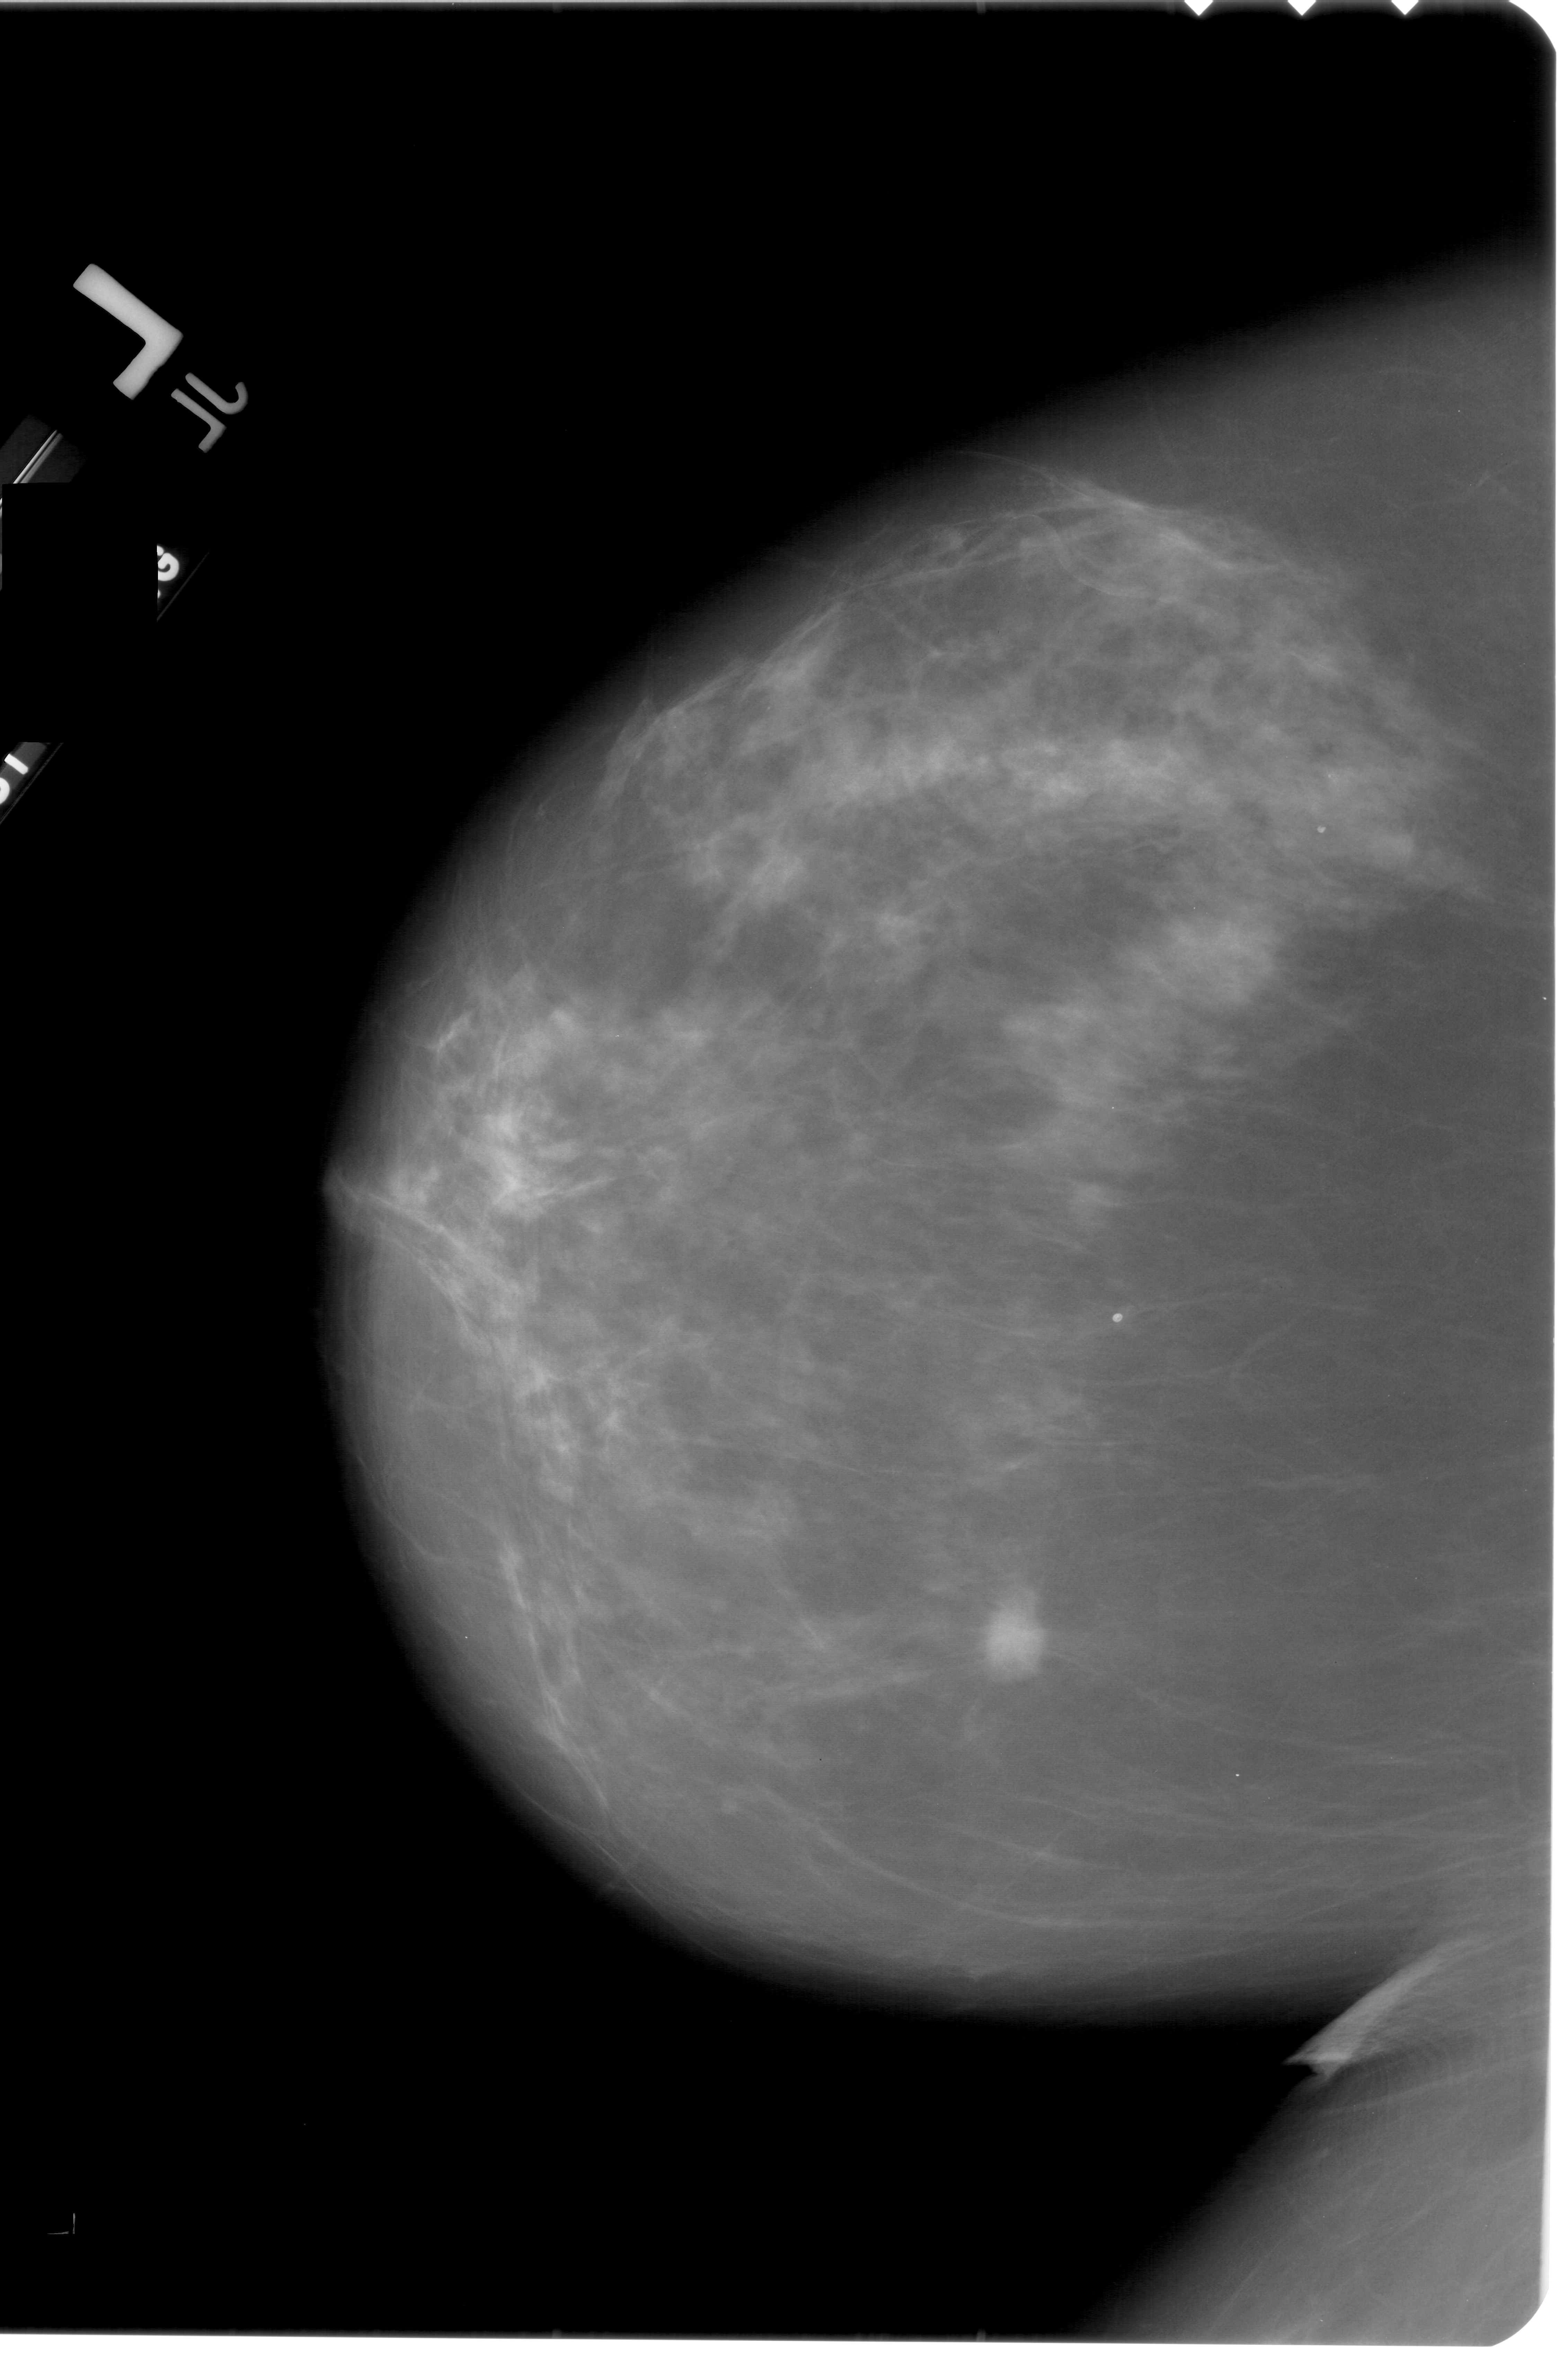
Scanned film-screen mammogram, left breast, CC view, breast composition: heterogeneously dense (BI-RADS density category 3 of 4).
- Marked abnormality: mass, shape irregular, margins spiculated; BI-RADS assessment category 5; subtlety rating 5 on a 1 (subtle) to 5 (obvious) scale; pathology (as recorded): malignant.